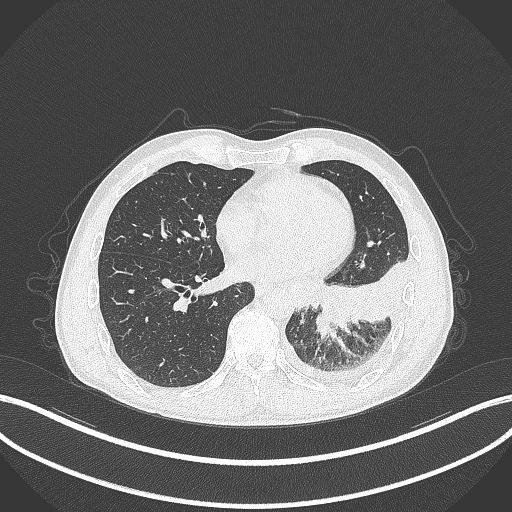
Chest CT, one axial slice; slice 116 of 295 in the series (ordered by position); reconstruction kernel B70f; lung window (W 1500 / L -600 HU); 1 mm slice thickness; 512 × 512 image matrix, field of view 400 × 400 mm. Patient: male, 47 years. Case-level facts recorded for this patient, not image findings: clinical TNM (as recorded): T3 N1 M1c; histopathological grade: G3.
Outlined on this slice (rectangle marked by the reading radiologist):
- lung tumour (recorded histology: small cell carcinoma): bounding box (x1, y1, x2, y2) in pixels: (311, 307, 337, 341)